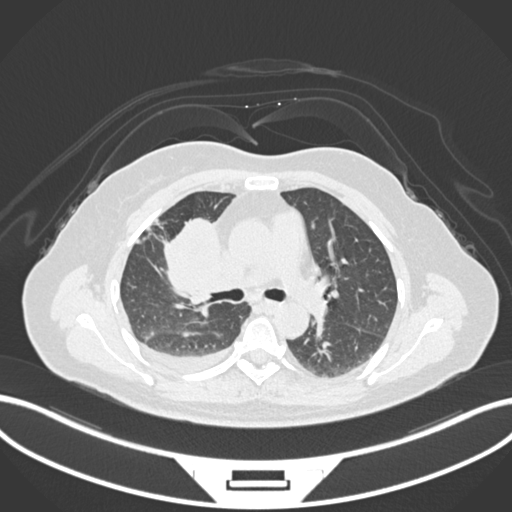
Chest CT, one axial slice; slice 90 of 172 in the series (ordered by position); reconstruction kernel B30f; lung window (W 1500 / L -600 HU); 1 mm slice thickness; 512 × 512 image matrix, field of view 400 × 400 mm. Female patient, age 52 years. Case-level facts recorded for this patient, not image findings: clinical TNM (as recorded): T3 N1 M1.
Annotated regions visible in this slice (rectangle marked by the reading radiologist):
- lung tumour (recorded histology: adenocarcinoma): bounding box [x1, y1, x2, y2] px = [164, 213, 223, 303]